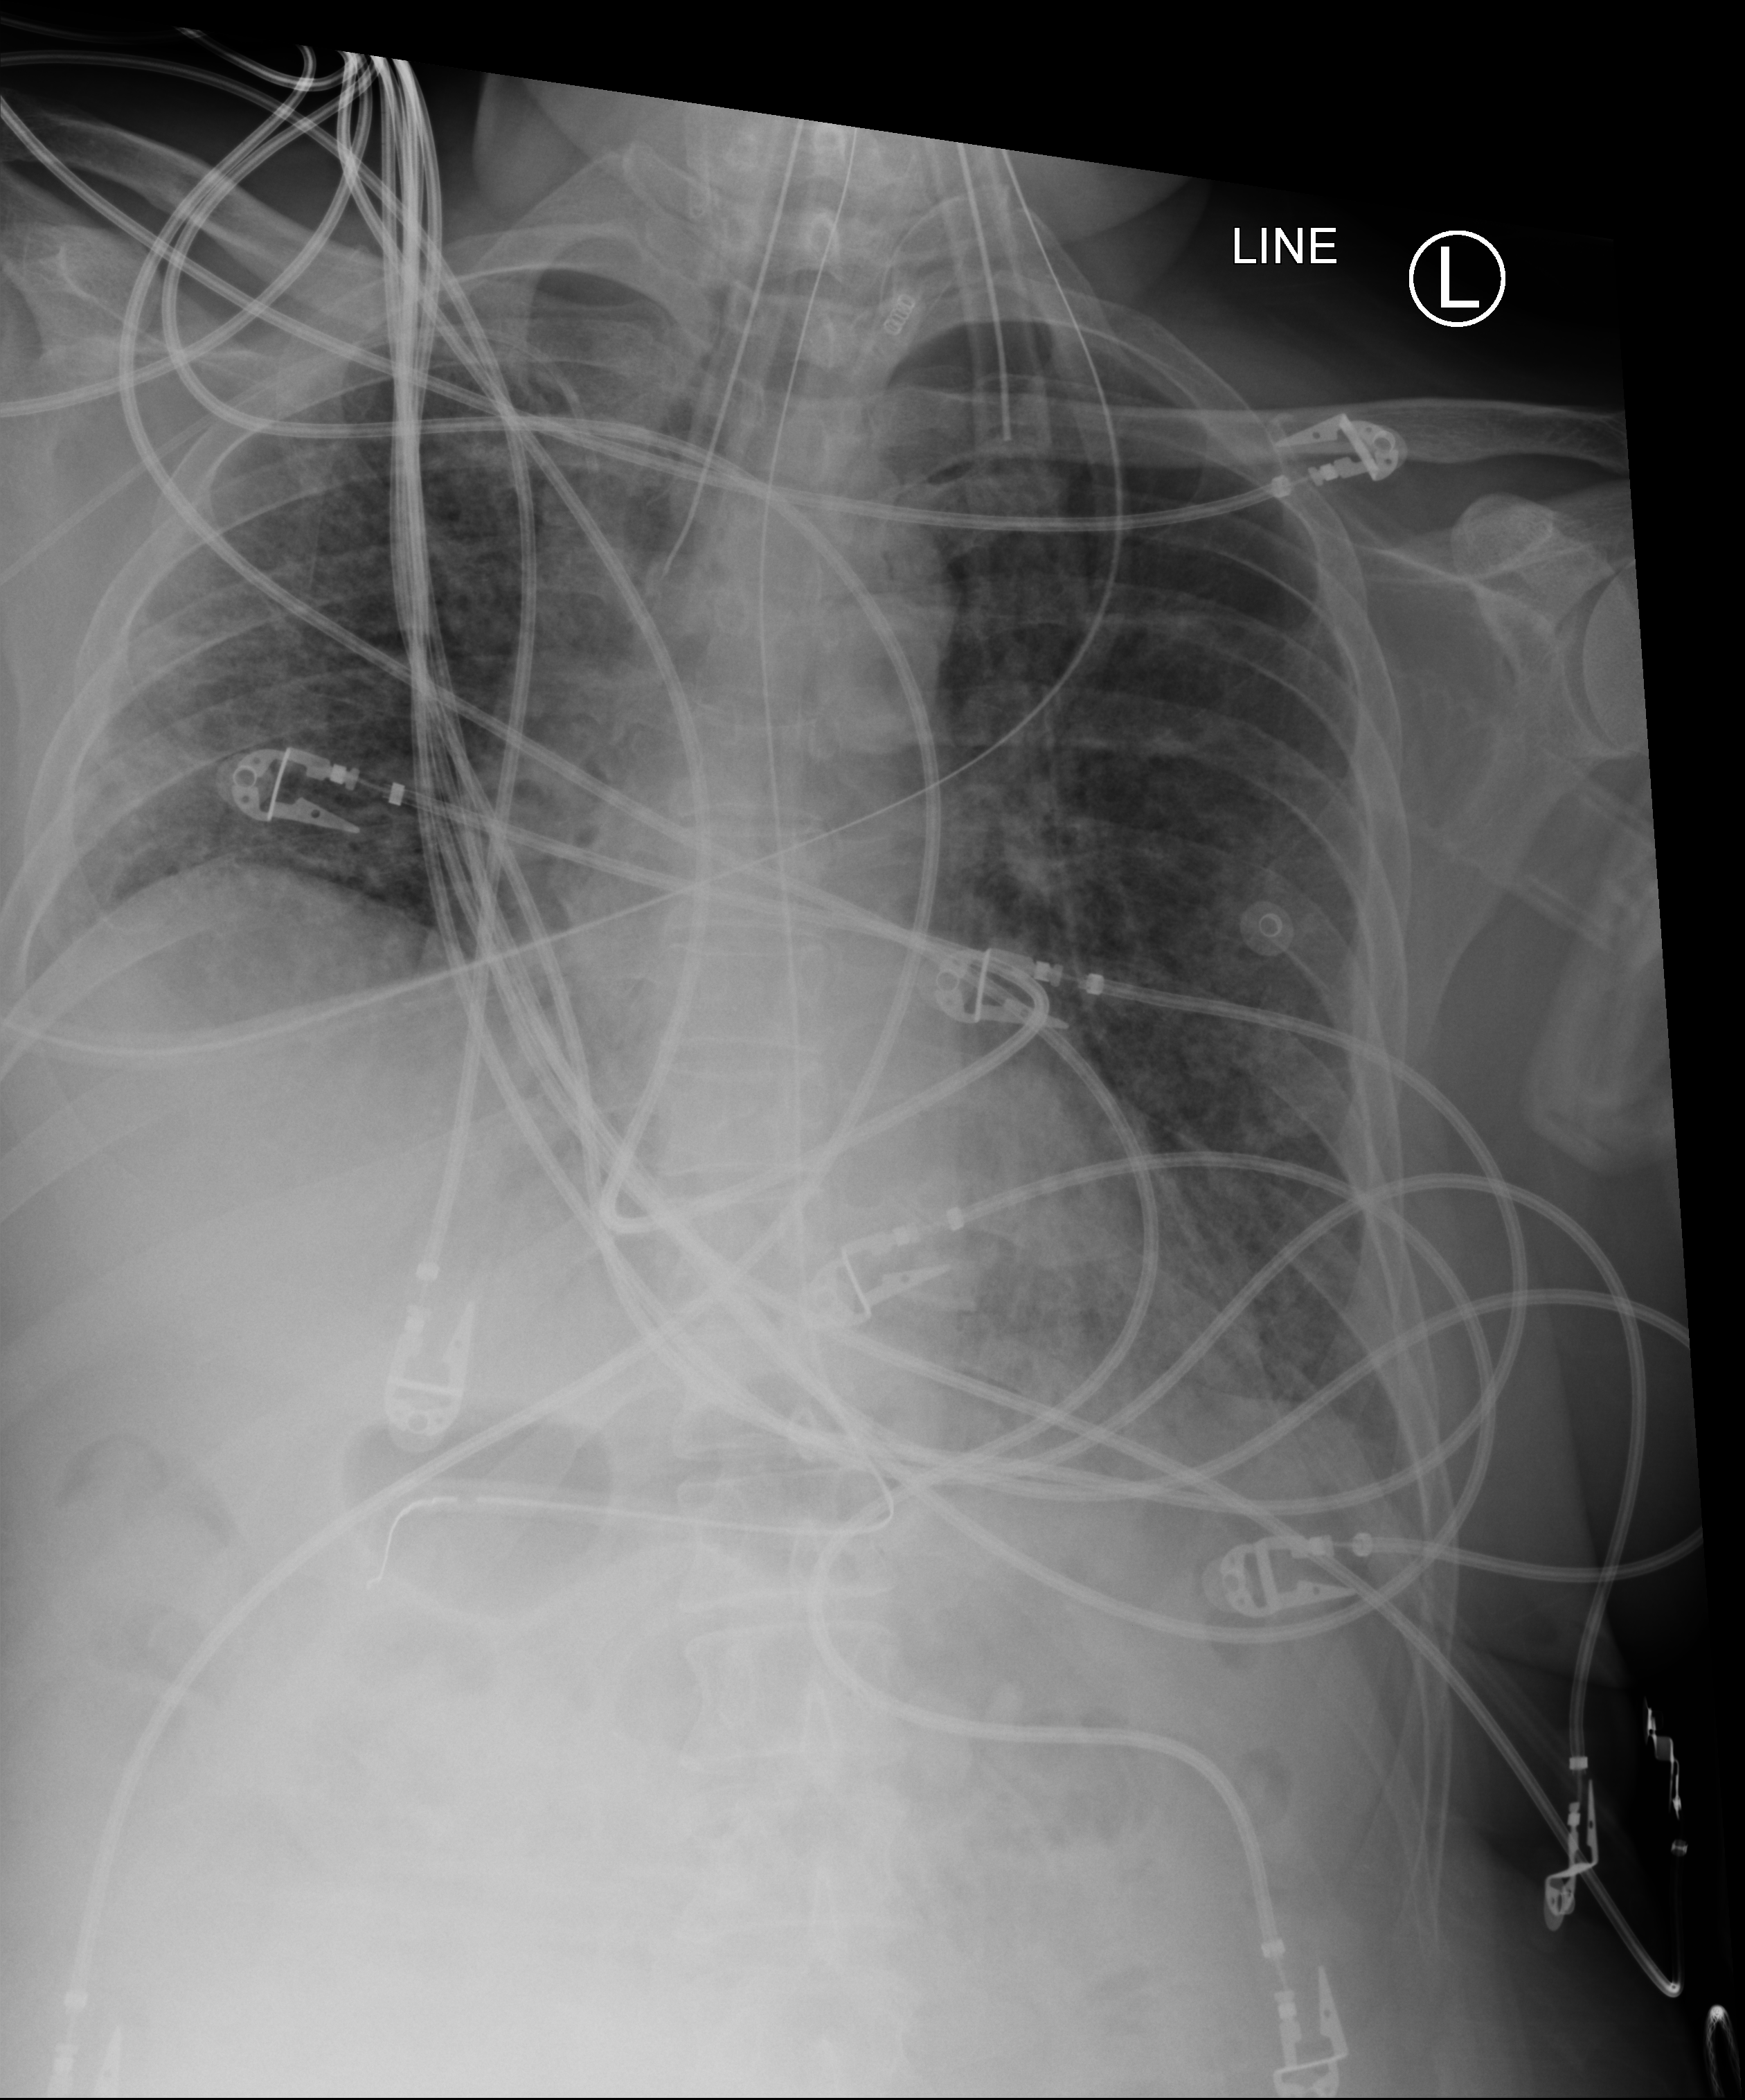
Chest X-ray (portable); anteroposterior (AP) projection. Patient hospitalised with COVID-19; male, aged 18–59 years.
From the hospital-stay record, not from the radiograph (when in the stay this image was taken is not recorded): admitted to intensive care during this hospital stay: yes; mechanically ventilated during this hospital stay: yes.